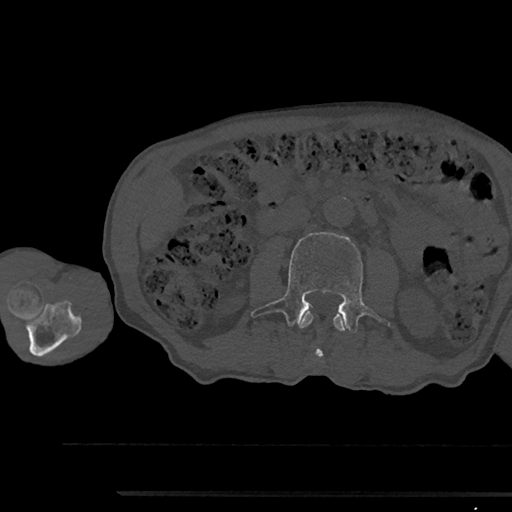
CT including the spine, one axial slice; slice 509 of 797 in the series (ordered by position); reconstruction kernel Br40s/3; 120 kVp; bone window (W 1800 / L 400 HU); 0.5 mm slice thickness; 512 × 512 image matrix, field of view 367 × 367 mm. Male patient, age 79 years. From the clinical record (not read from this slice): primary cancer: prostate.
Structures marked on this image (semi-automatically segmented with operator editing):
- L2 vertebra: bounding box [x1, y1, x2, y2] px = [298, 312, 346, 359]
- L3 vertebra: [251, 232, 391, 331]